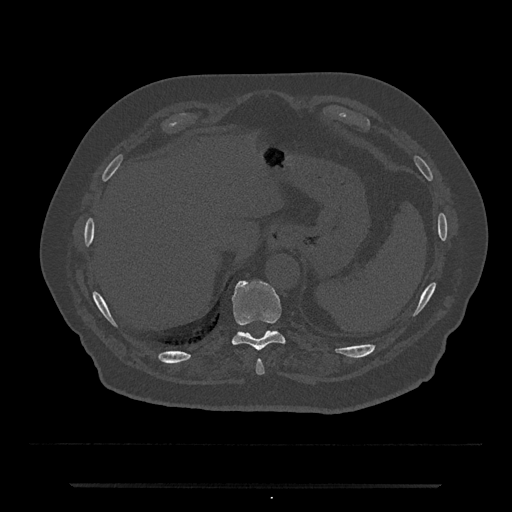
CT including the spine, one axial slice. Position 704 of 797 along the scan axis. Reconstruction kernel Br40s/3. 120 kVp. Bone window (W 1800 / L 400 HU). 512 × 512 image matrix, field of view 434 × 434 mm. Male patient, age 80 years. Case-level facts recorded for this patient, not image findings: primary cancer: prostate; vertebrae with lytic lesions (as recorded): L1, T11.
Outlined on this slice (semi-automatic segmentation, software-assisted and operator-edited):
- T10 vertebra: bounding box <231,280,285,351> (left, top, right, bottom; pixels)
- T9 vertebra: <256,360,265,375>